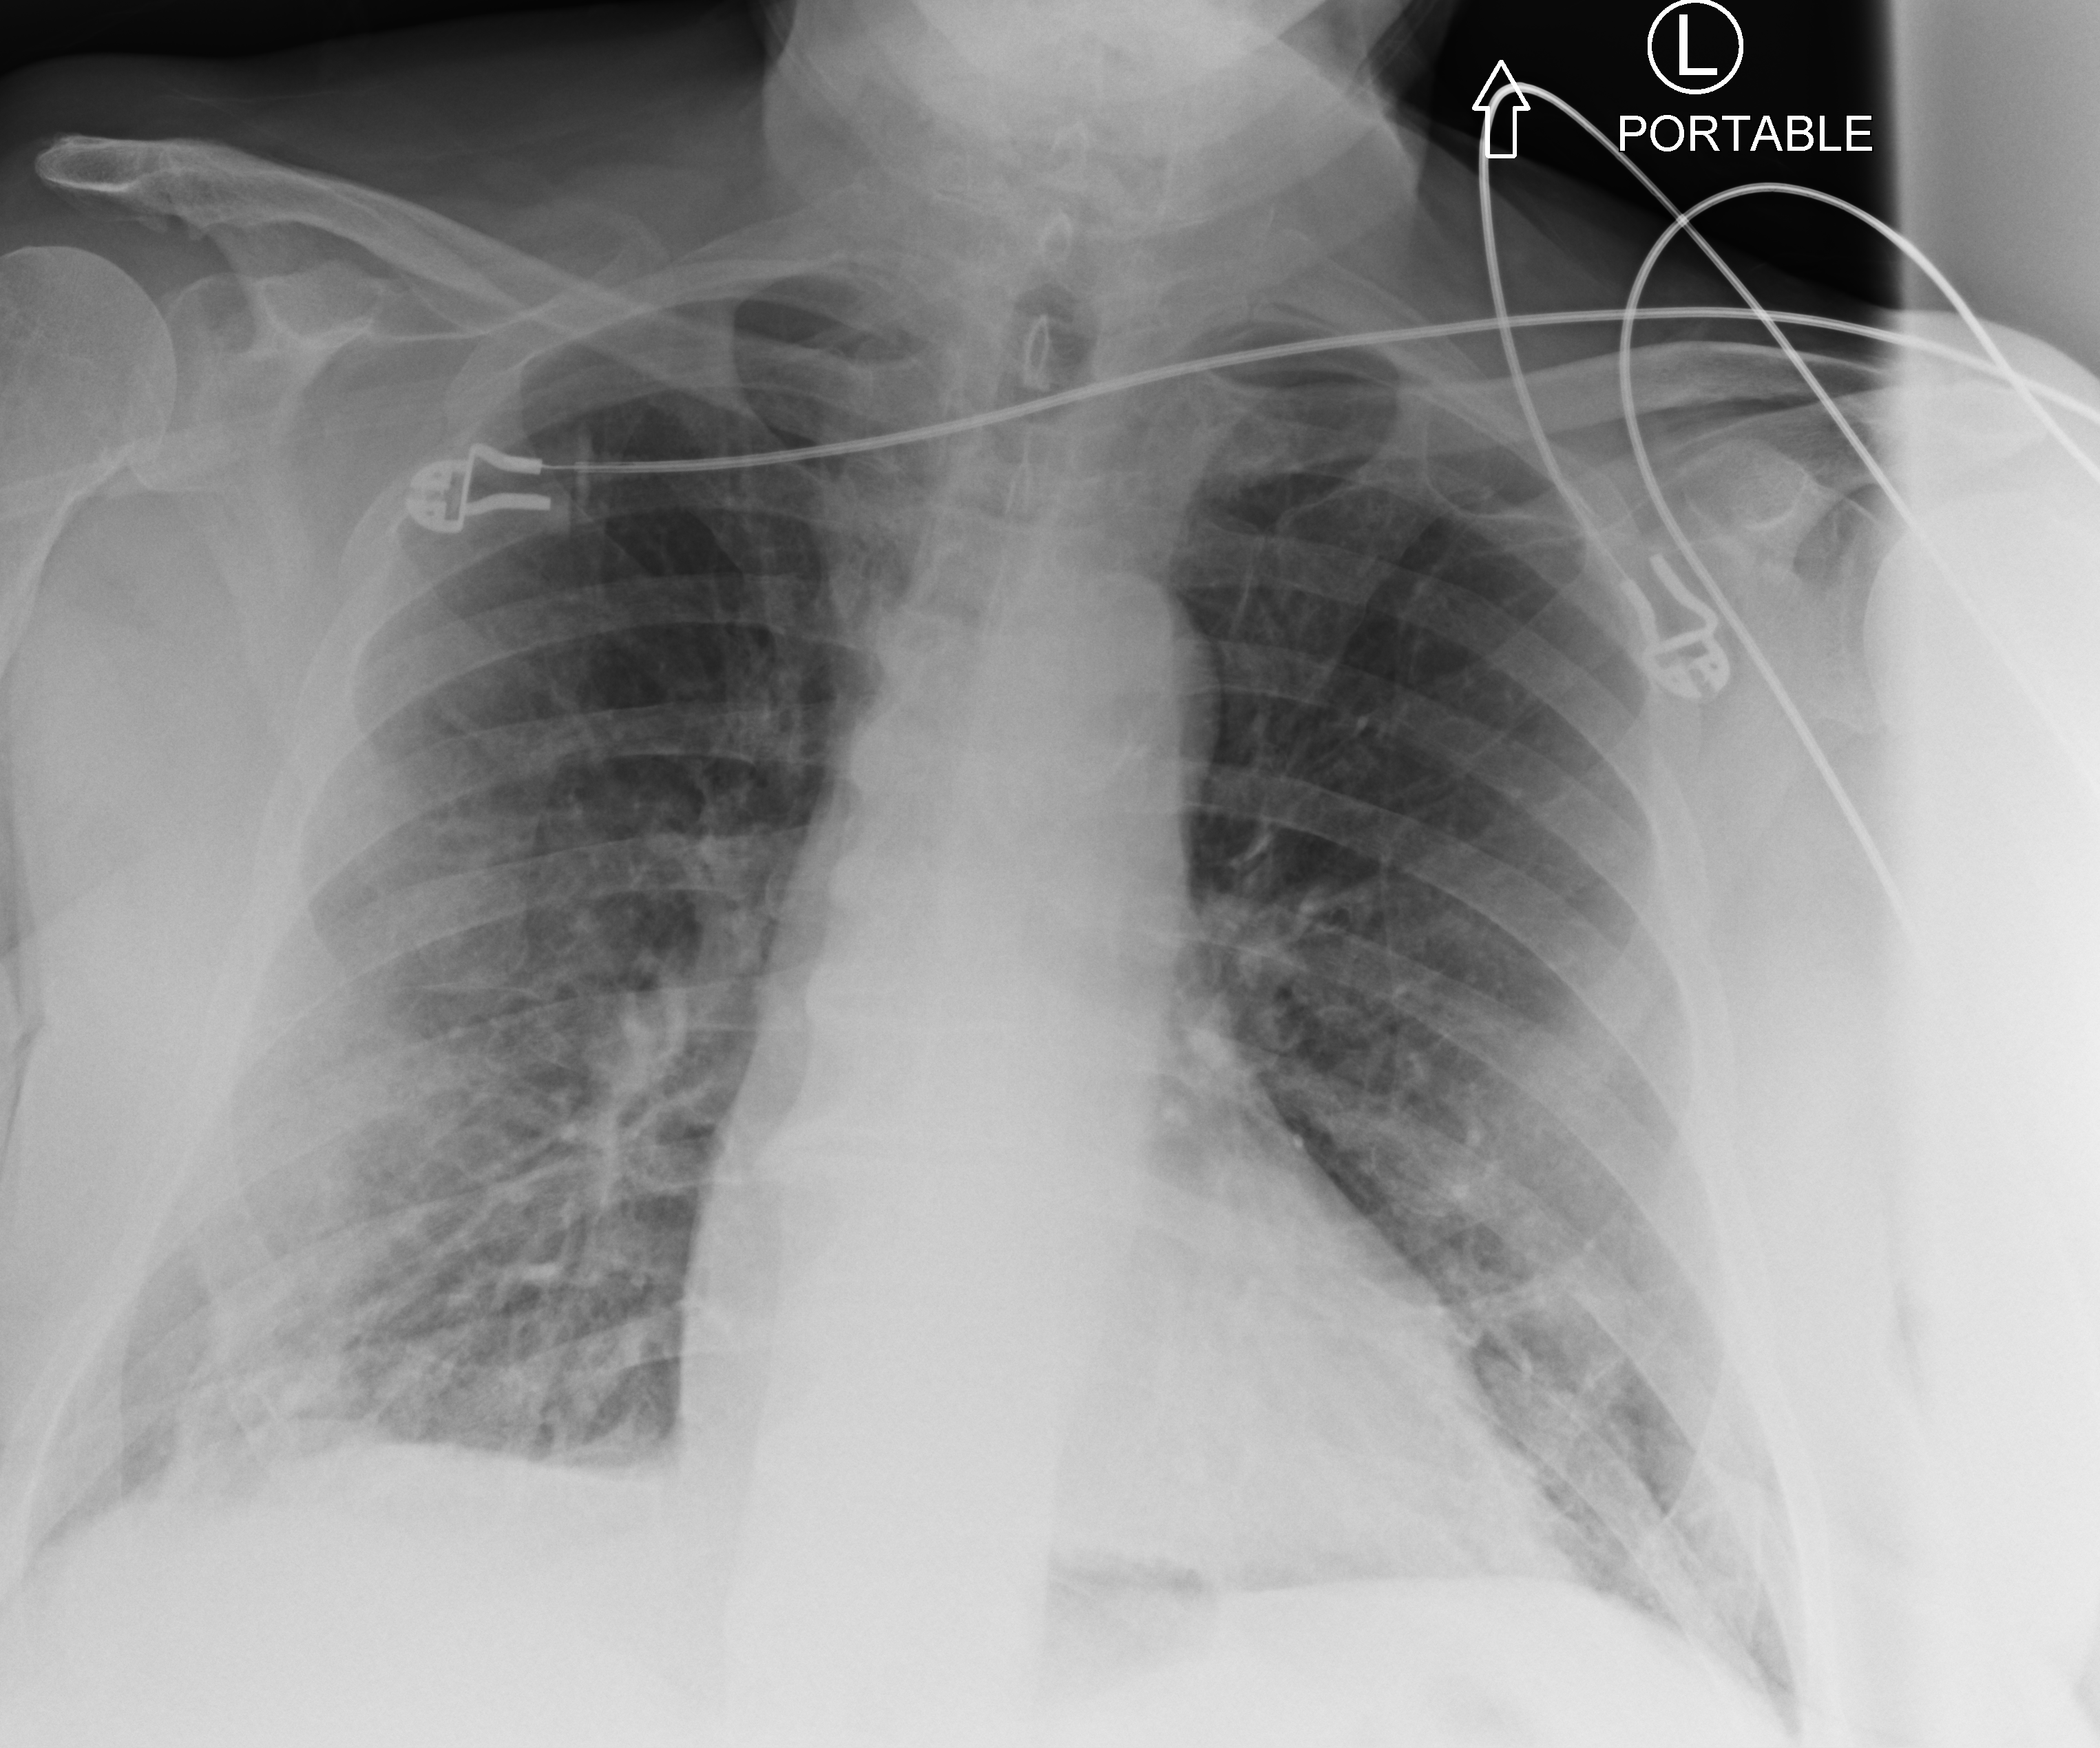
Chest X-ray (portable); anteroposterior (AP) projection. Patient hospitalised with COVID-19; male, aged 75–90 years.
Admission-level facts for this patient (not findings on this image; timing relative to this image not recorded): length of hospital stay: 3 days.